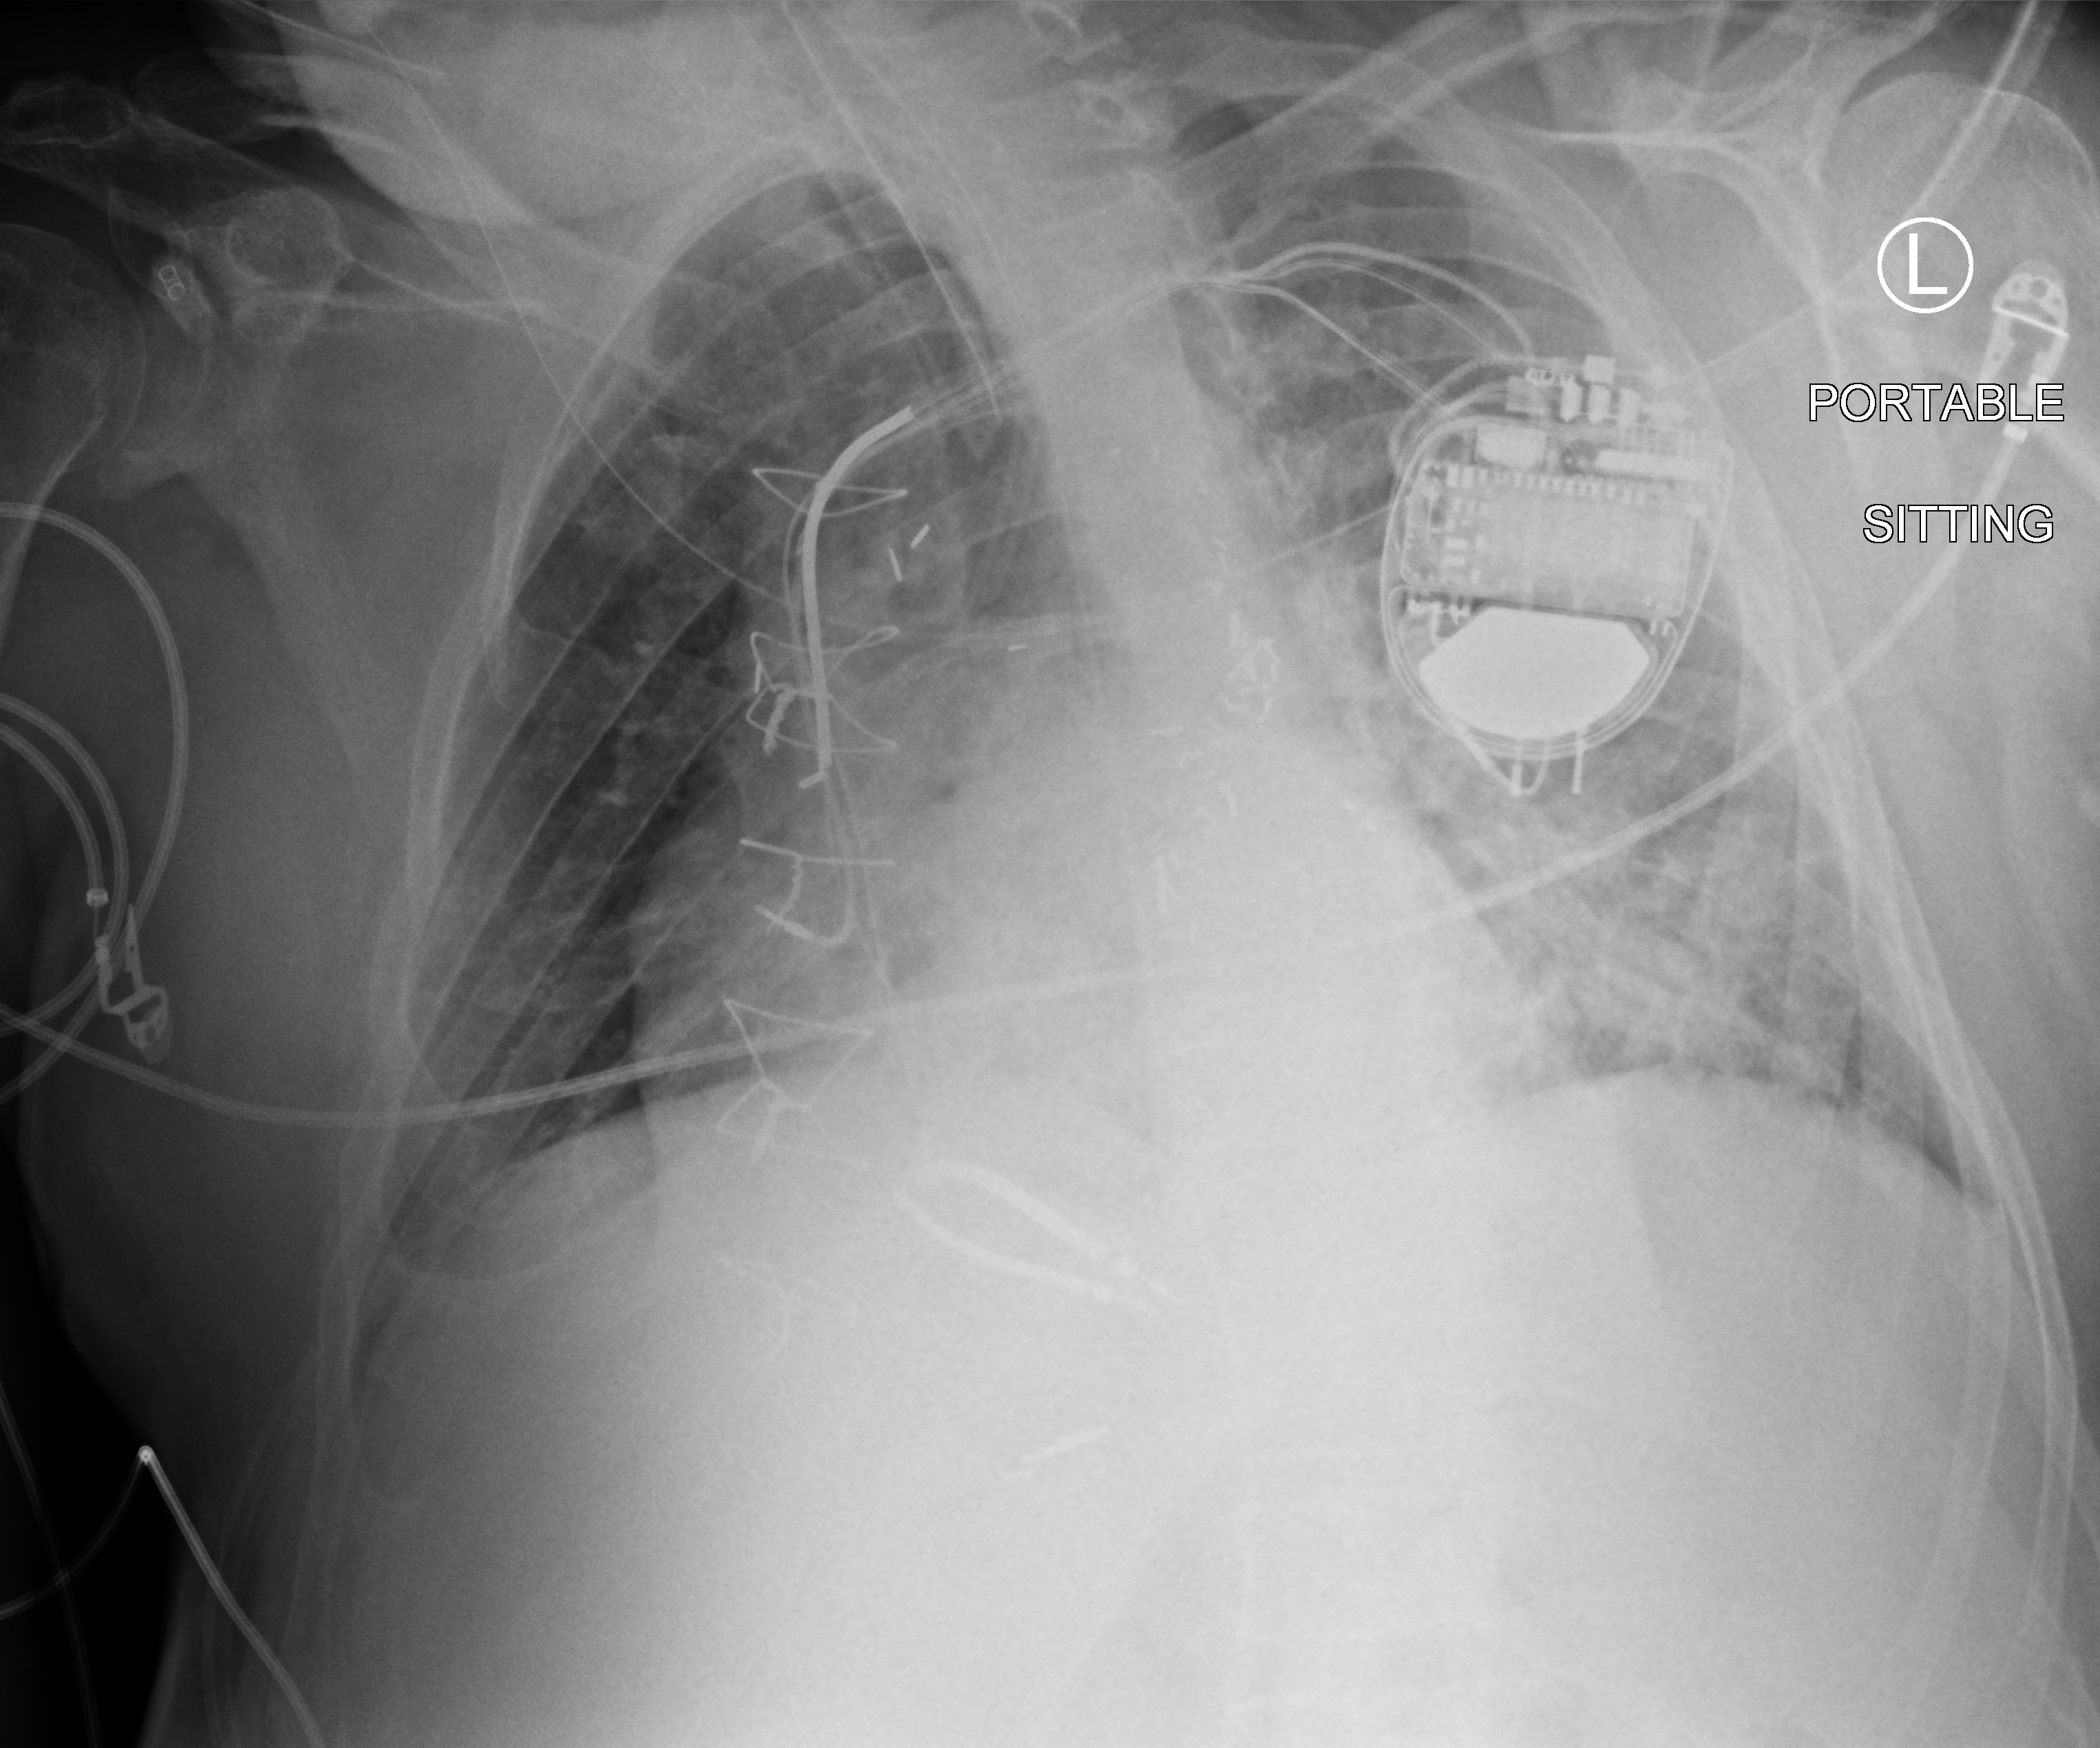
Bedside chest radiograph (computed radiography). Patient hospitalised with COVID-19; male, aged 60–74 years.
Hospital-stay facts (about this admission, not read from this image; timing relative to this image not recorded):
- mechanically ventilated during this hospital stay: yes
- admitted to intensive care during this hospital stay: yes